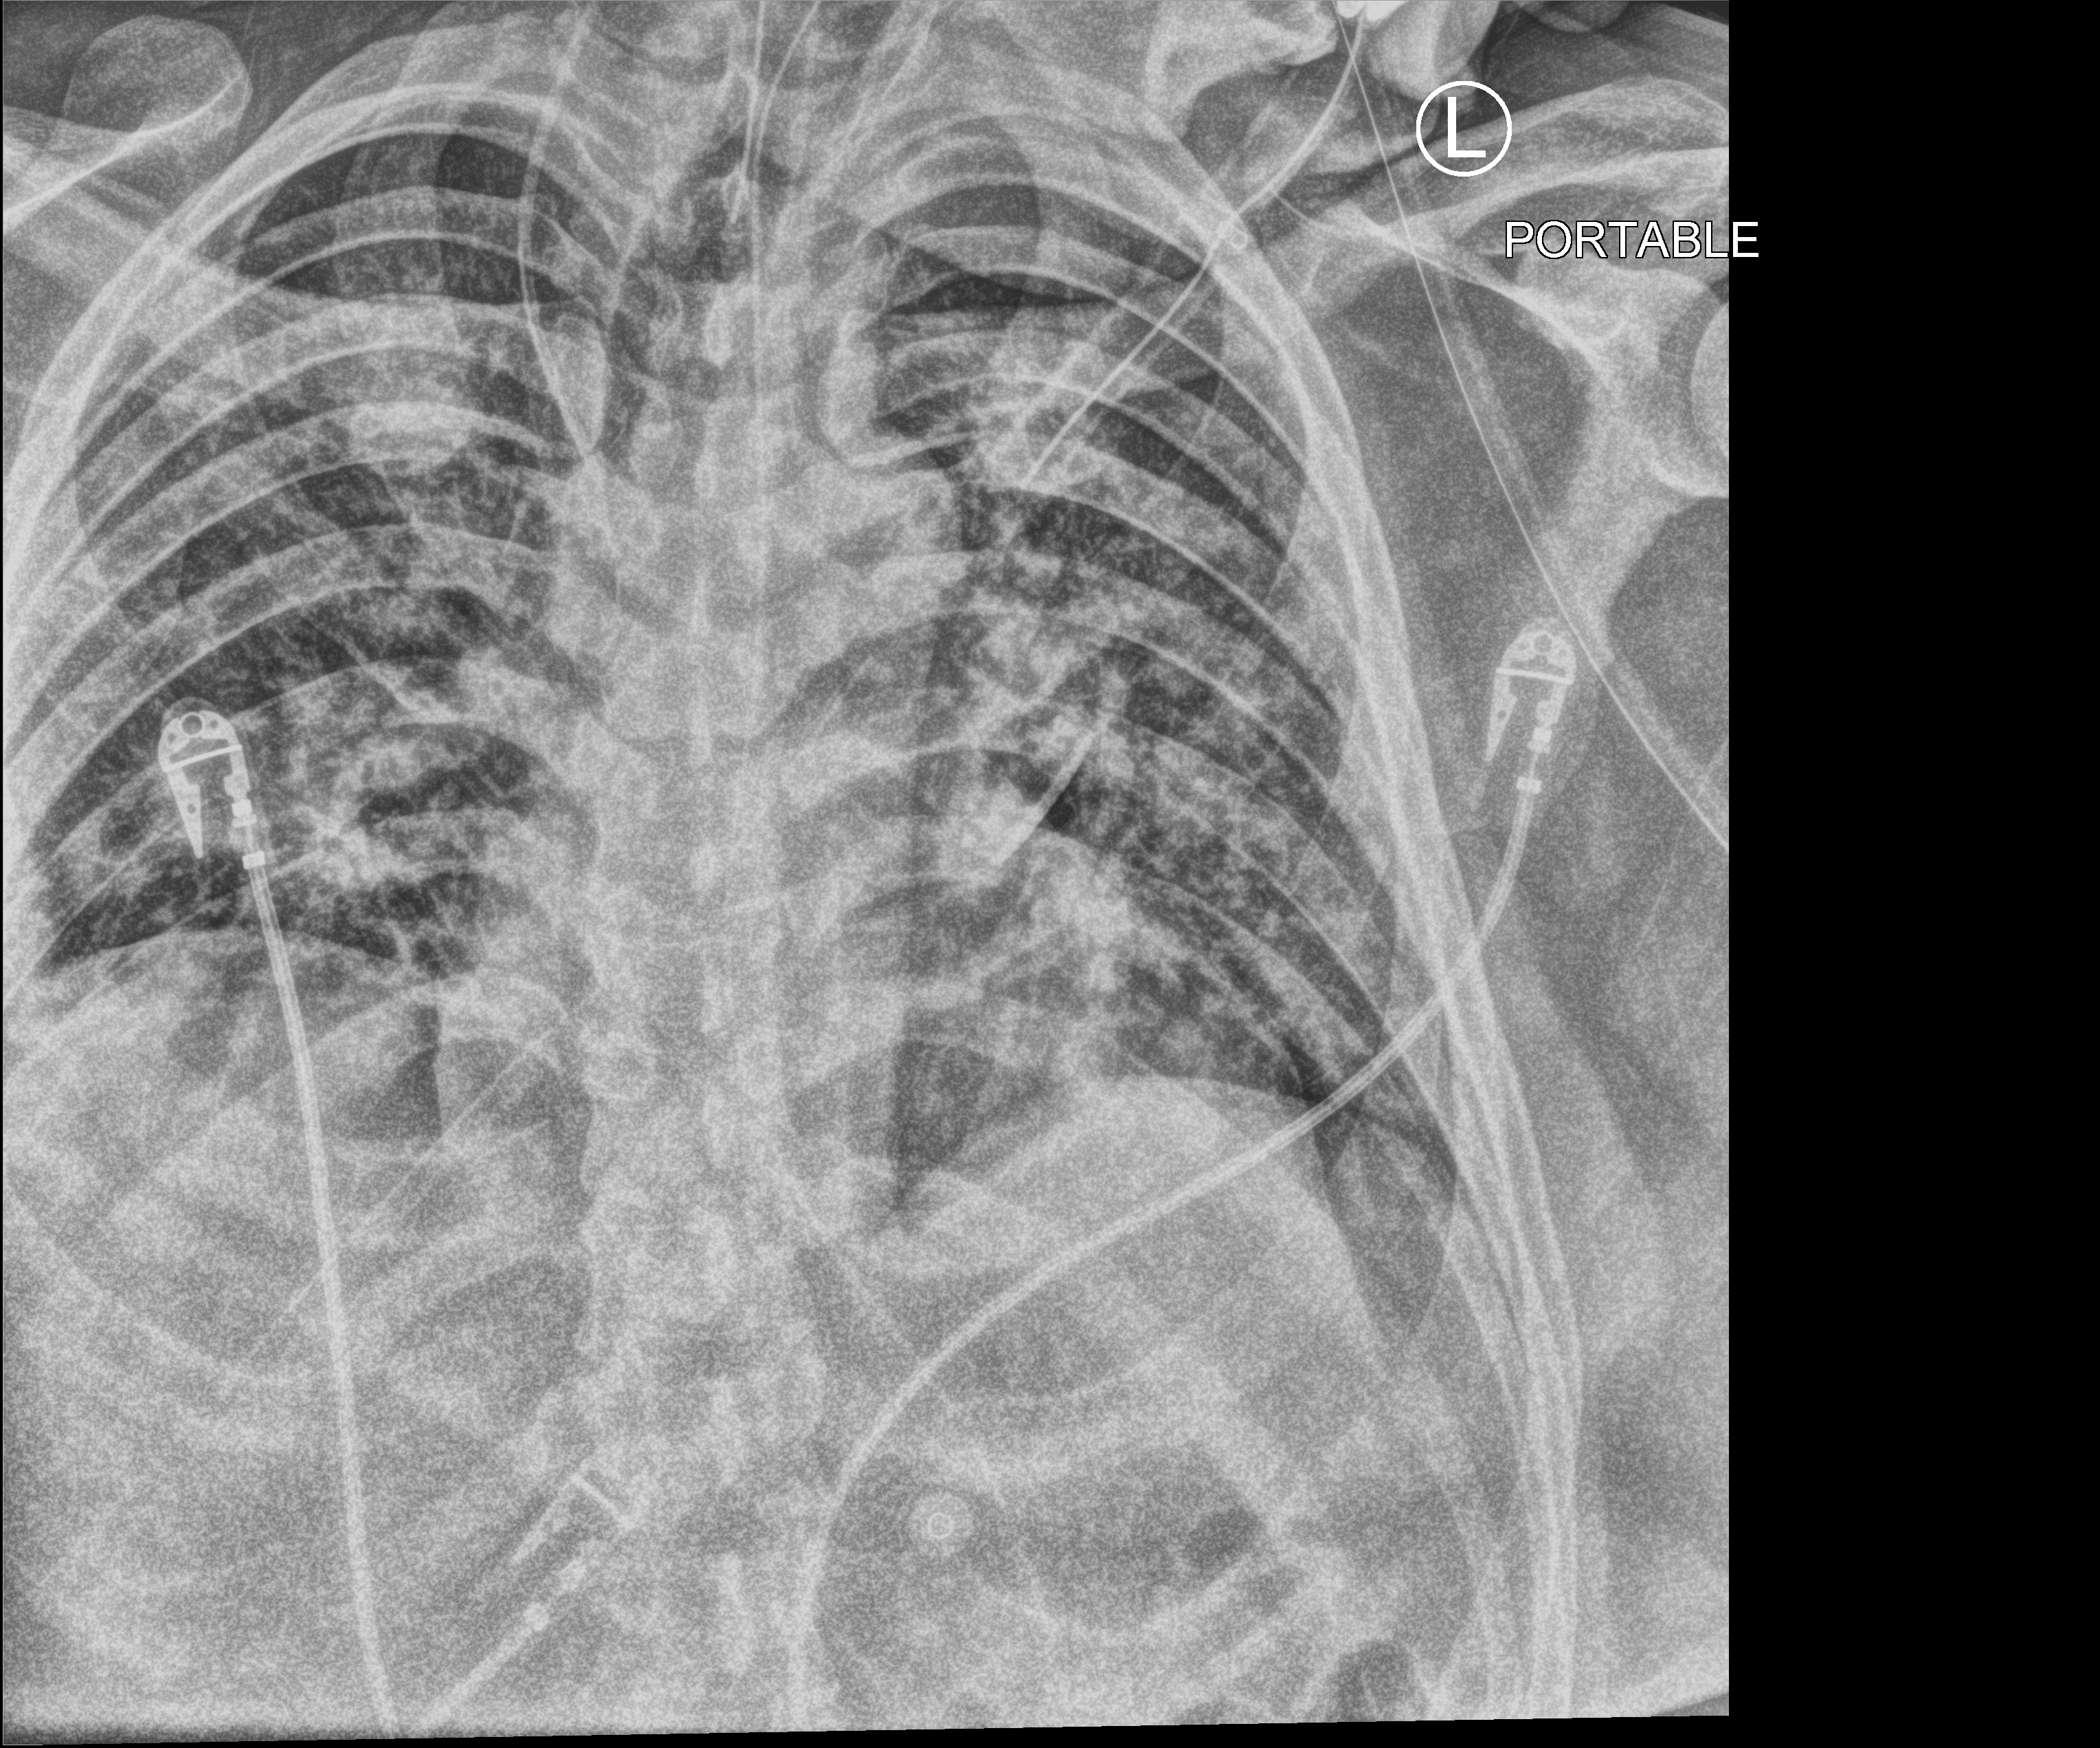
Bedside chest radiograph (computed radiography), anteroposterior (AP) projection. Male patient hospitalised with COVID-19, age 18–59 years.
Hospital-stay facts (about this admission, not read from this image; timing relative to this image not recorded):
- admitted to intensive care during this hospital stay: yes